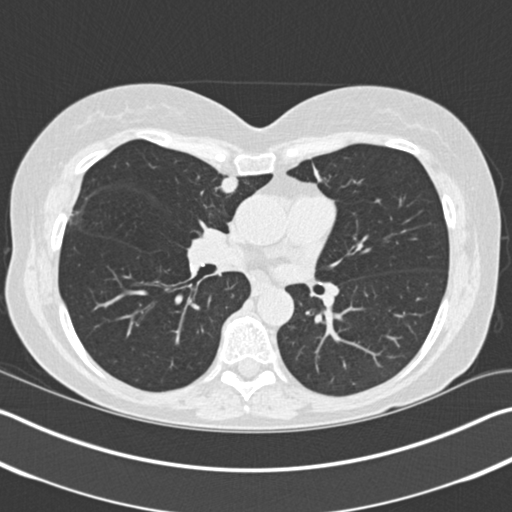
Chest CT (low-dose screening protocol), one axial image, baseline annual screen, lung window (W 1500 / L -600 HU), 2 mm slice thickness, 120 kVp, slice 86 of 183 in the series, 512 × 512 image matrix, field of view 340 × 340 mm. Female, age 61 years at enrolment. Former smoker at enrolment.
- Expert reader's lesion annotation, bounding box [x1, y1, x2, y2] px = [201, 169, 246, 209].
- The screening reader recorded 2 non-calcified nodules or masses ≥4 mm on this exam; which of them this box marks is not recorded.
- Official screen result: positive, change unspecified: nodule(s) >= 4 mm or enlarging nodule(s), mass(es), or other non-specific abnormalities suspicious for lung cancer.